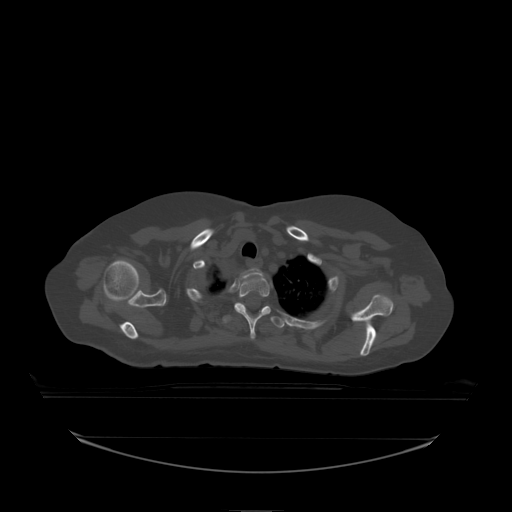
CT including the spine, one axial slice. Position 179 of 242 along the scan axis. Bone window (W 1800 / L 400 HU). 2.5 mm slice thickness. 512 × 512 image matrix, field of view 500 × 500 mm. Patient: female, 53 years. From the clinical record (not read from this slice): primary cancer: lung; vertebrae with lytic lesions (as recorded): T7, L1.
Annotated regions visible in this slice (semi-automatically segmented with operator editing):
- T1 vertebra: box from (x=241, y=268) to (x=263, y=279) px
- T2 vertebra: (x=235, y=276)–(x=271, y=338)
- T3 vertebra: (x=223, y=303)–(x=285, y=328)